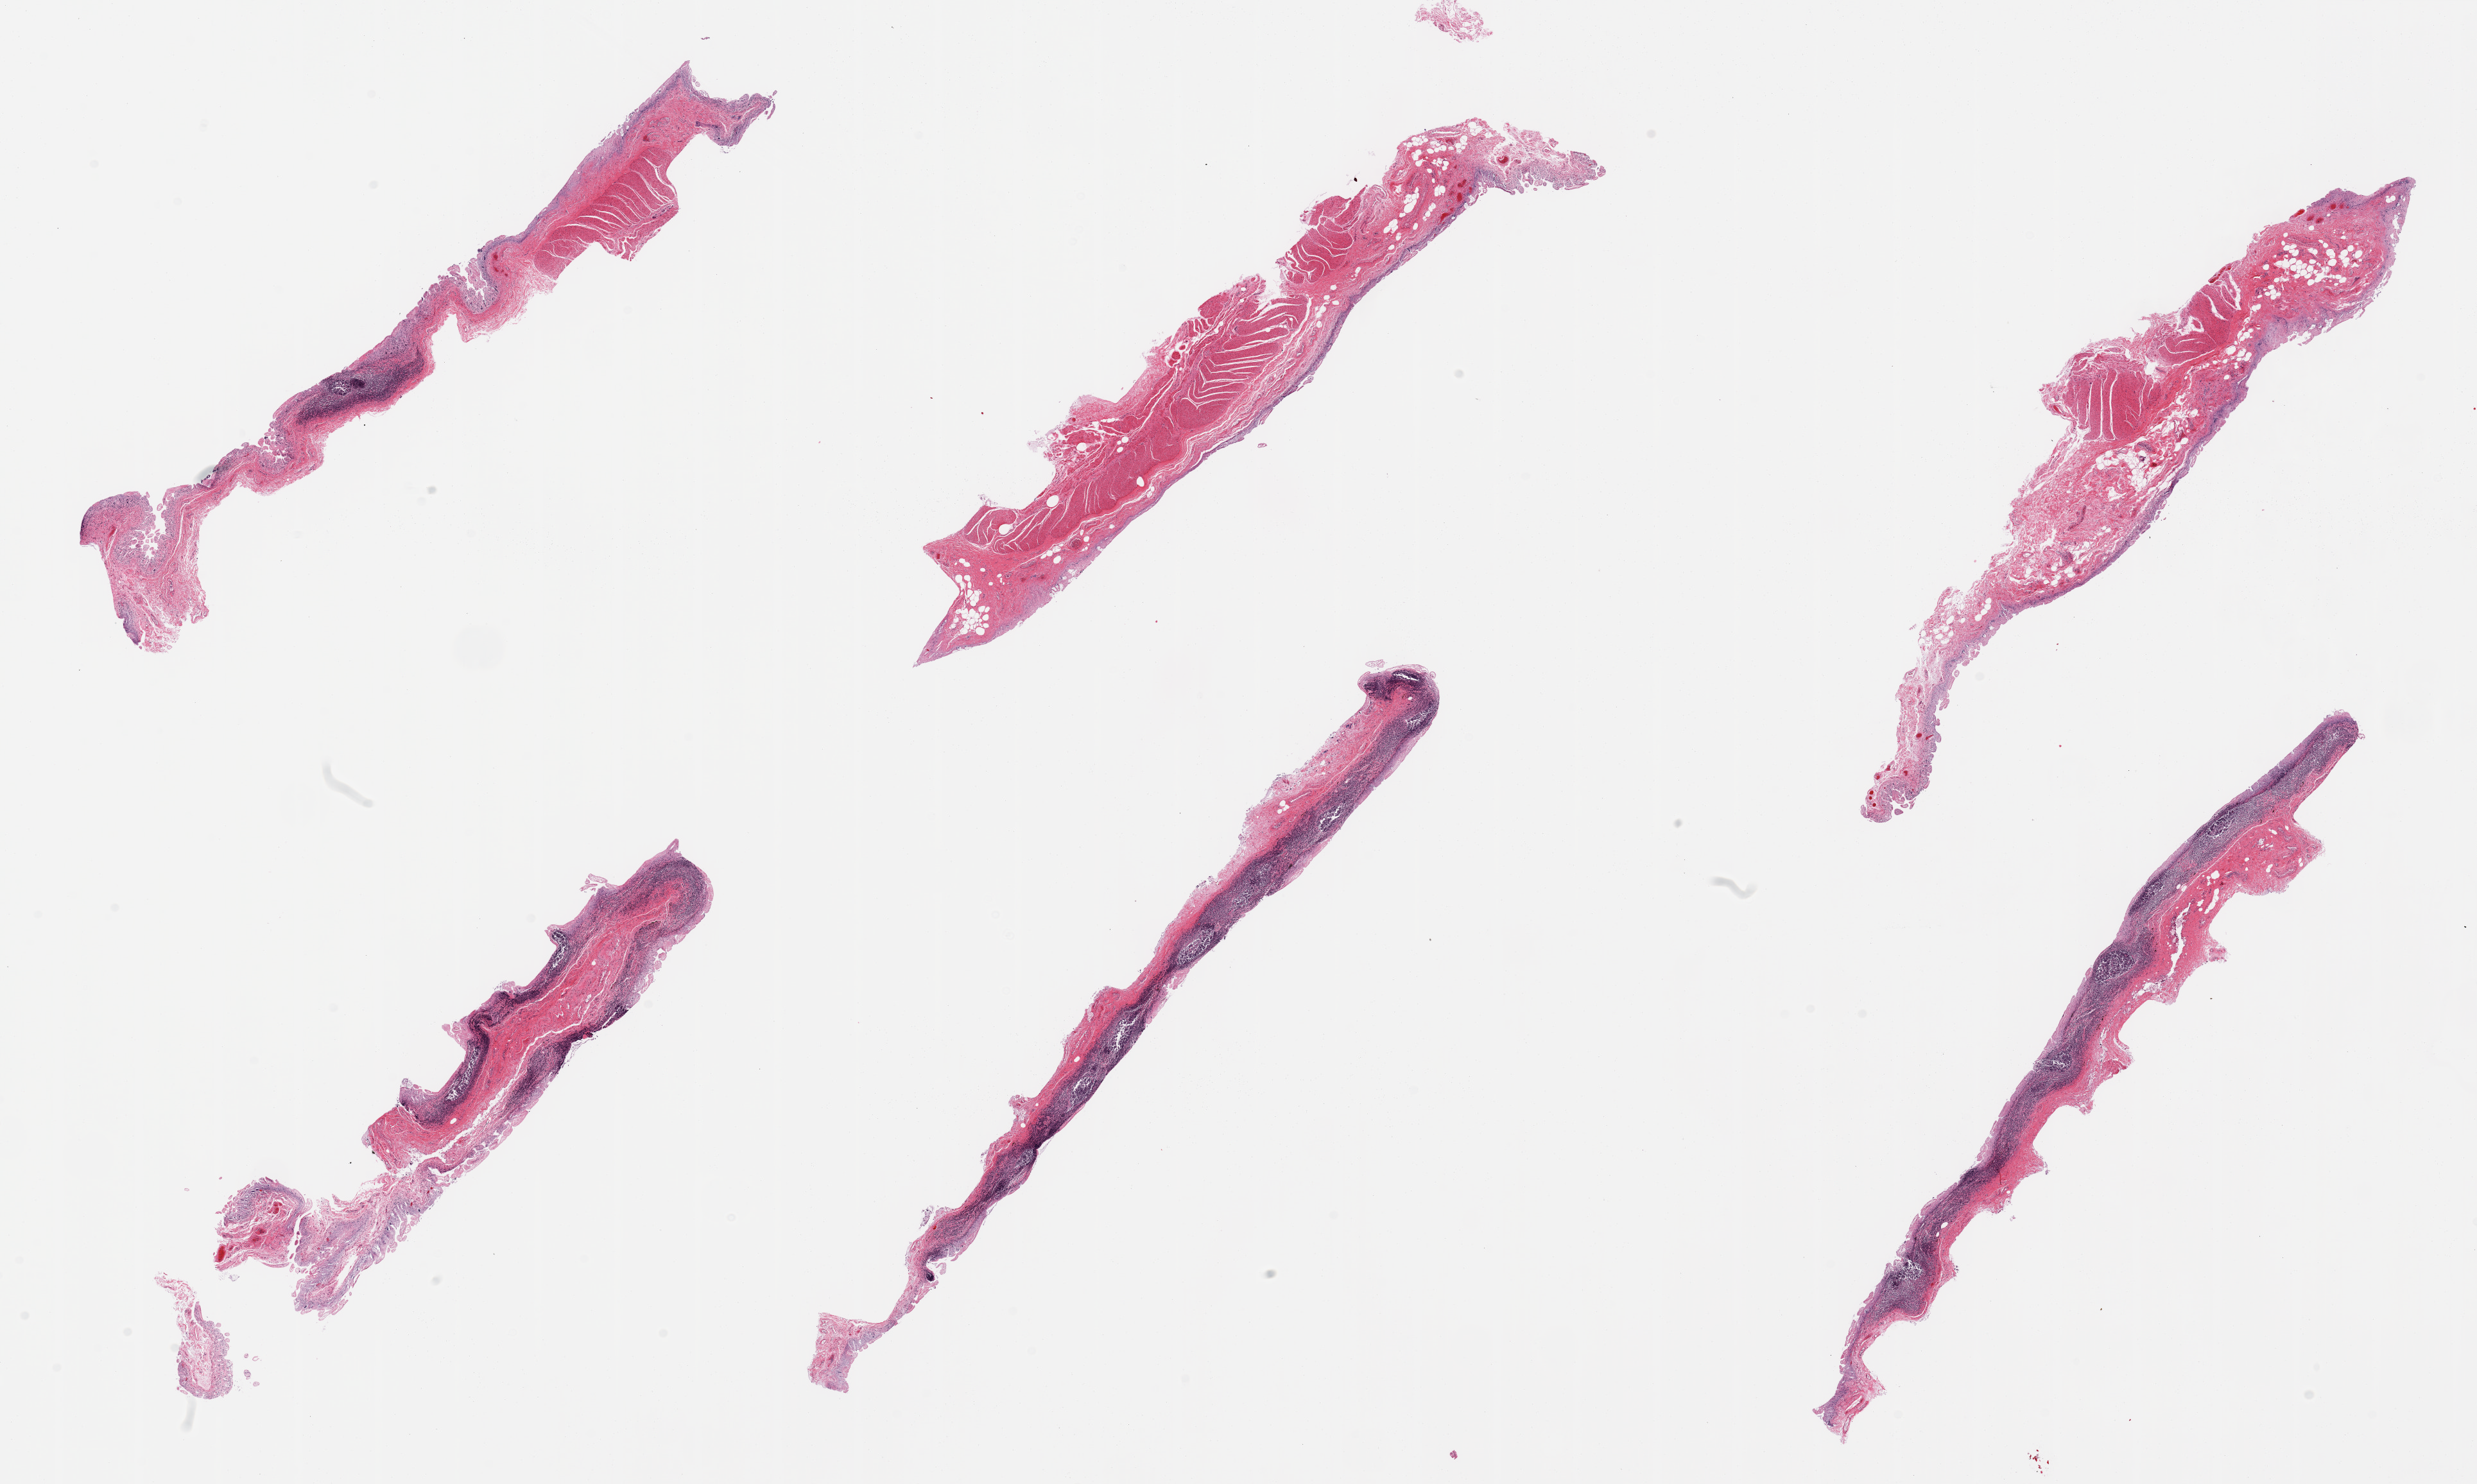
Whole-slide image, haematoxylin and eosin stain, a low-resolution overview of the entire scanned area, about 30.5 x 18.3 mm; PAXgene-fixed, paraffin-embedded tissue; sampled site (target tissue): ileum; tissue donor sample. Donor sex: male.
Reviewer comment on this tissue sample: 6 pieces; lymphoid tissue; mucosa completely autolyzed.